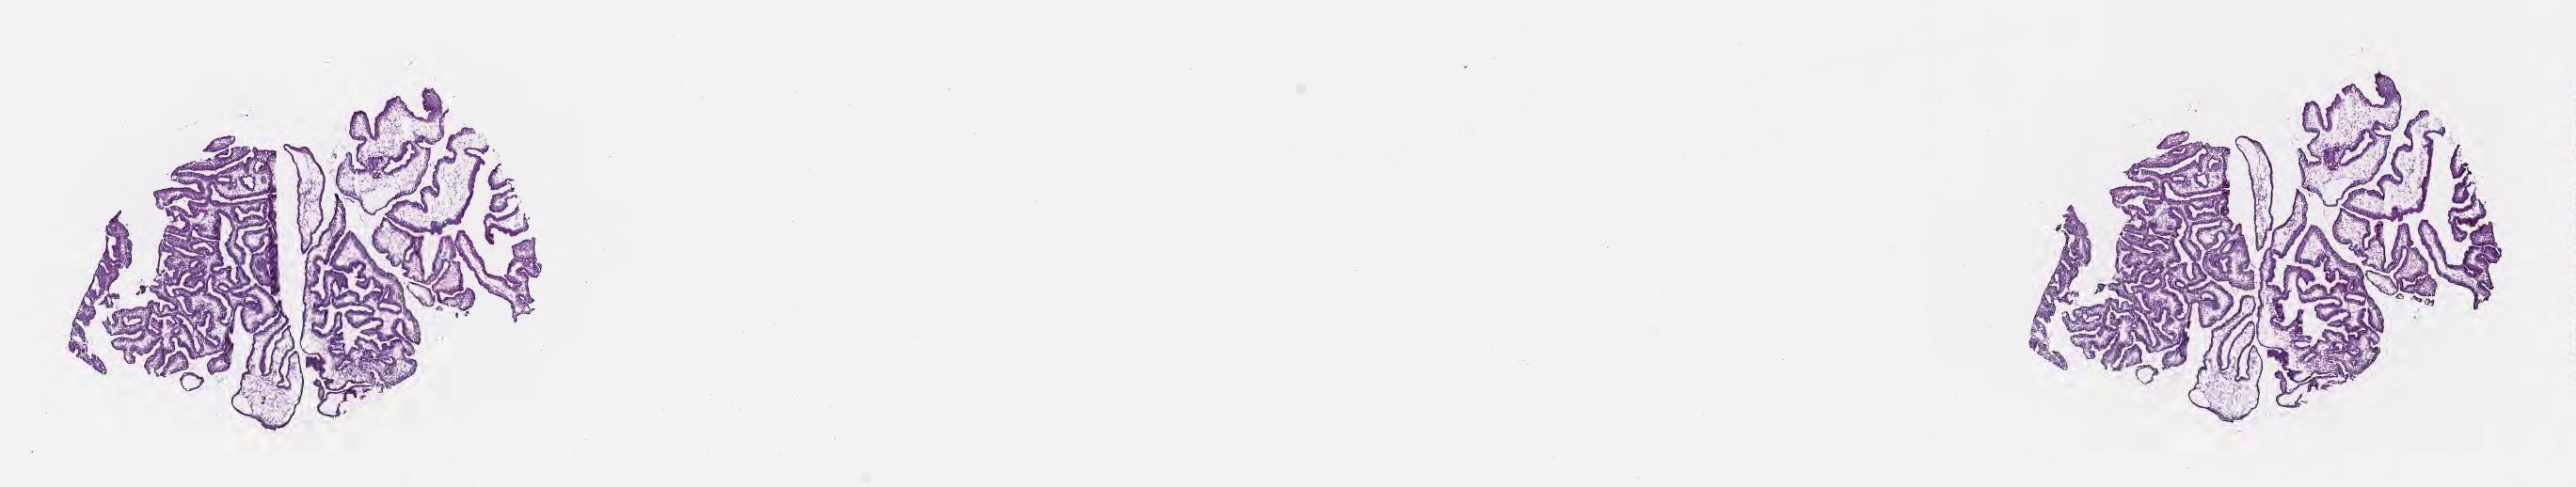
Digitized haematoxylin and eosin-stained section — low-resolution overview of the scanned area, about 22.1 x 4.2 mm, cryosection, primary tumor, anatomic site: duodenum. Patient: female, age at initial diagnosis 59 years. Composition of this section per pathologist review: tumor cells 85%, tumor nuclei 85%, stromal cells 15%, necrosis 0%, normal cells 0%. Inflammatory infiltration, as recorded: lymphocyte infiltration 5%, monocyte infiltration 2%, neutrophil infiltration 3%.
Section: bottom of the tissue portion. Histologic diagnosis: Tubulovillous adenoma, NOS. AJCC pathologic stage: Stage I.